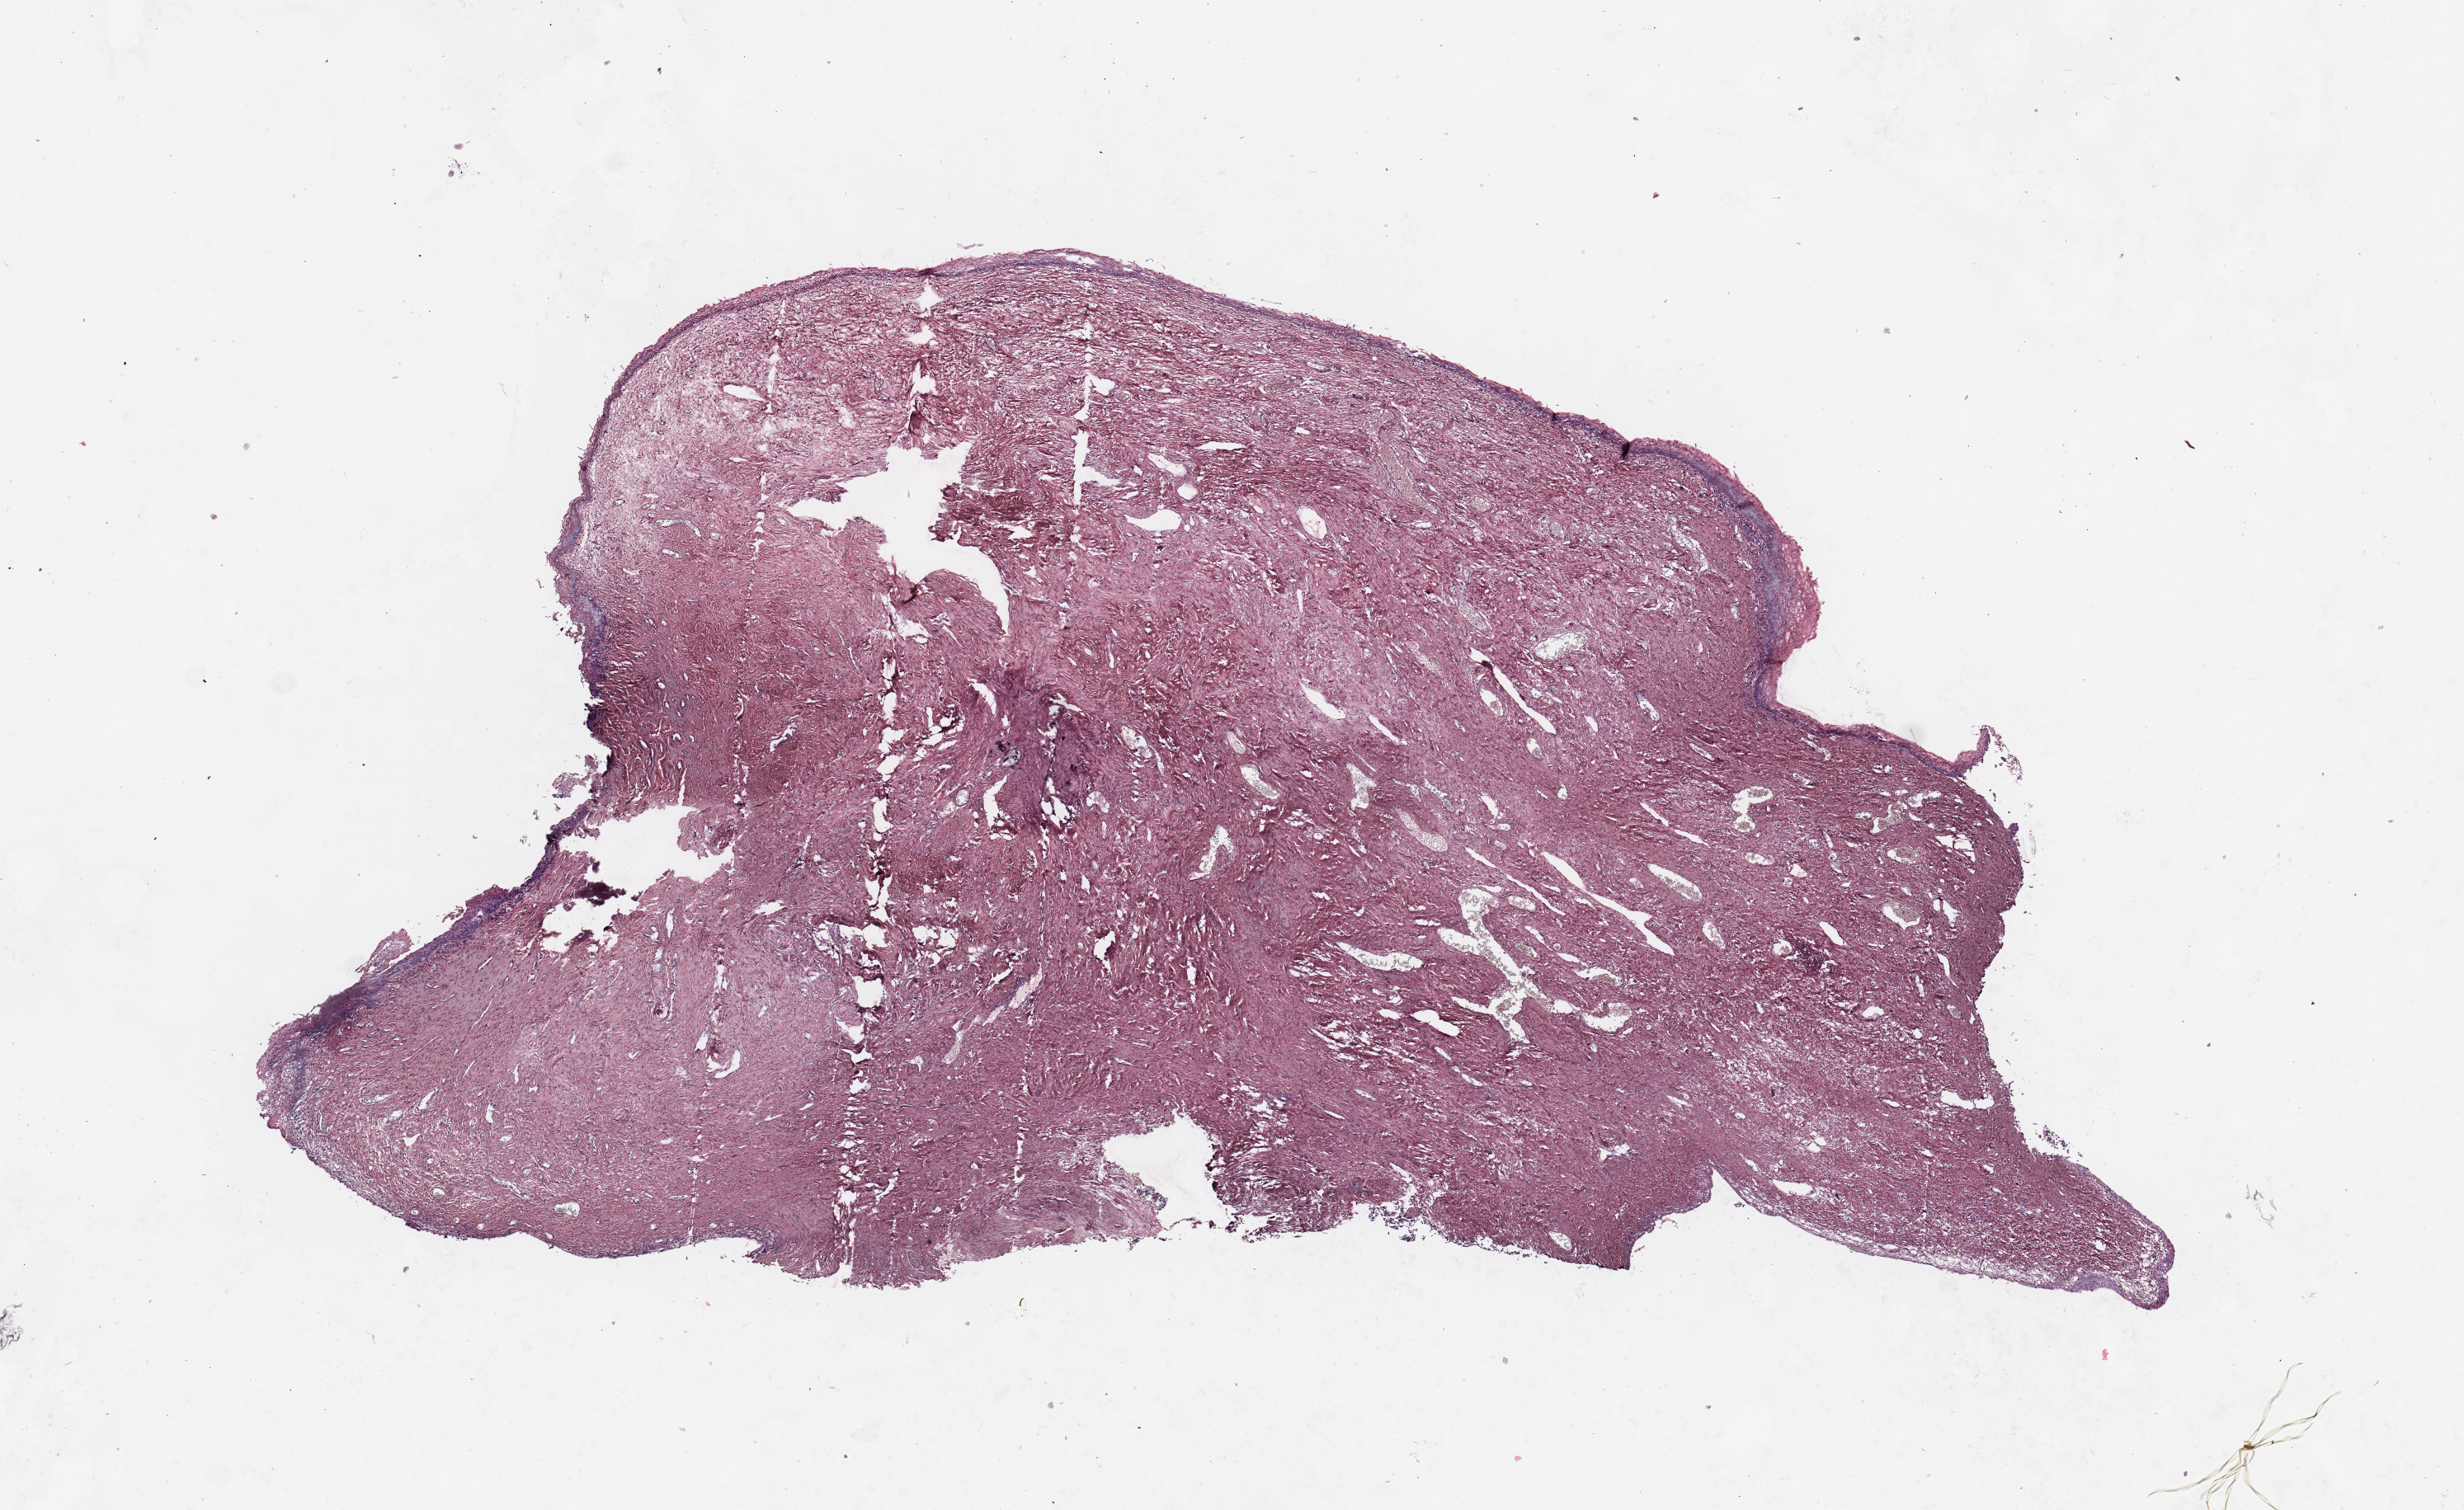
Digitized H&E-stained tissue section (whole slide) — whole scanned area (about 11.8 x 7.2 mm) shown as a low-resolution overview. Uterus, normal (non-tumour) tissue. Female, 70 y/o.
This section: normal (non-tumour) tissue from the same patient. Patient diagnosis: Endometrioid adenocarcinoma, NOS.